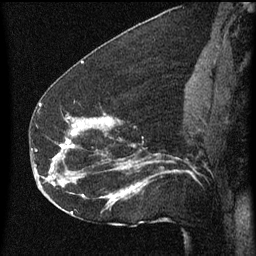
Breast MRI (dynamic contrast-enhanced), one sagittal slice. Dynamic contrast-enhanced series, image 2 of 3 at this slice position (ordered by acquisition). 1.5 T. TE 4.2 ms, TR 8 ms. 2 mm slice thickness. 256 × 256 image matrix. Female patient, age 52 years.
Structures marked on this image (semi-automatically segmented with operator editing):
- analysis volume of interest (the breast-tissue region the enhancement analysis was run in; not a lesion): bounding box (x1, y1, x2, y2) in pixels: (54, 112, 178, 207)
- tumour enhancement mask (voxels above the 70 % enhancement threshold inside the analysis volume of interest): (60, 118, 145, 197)